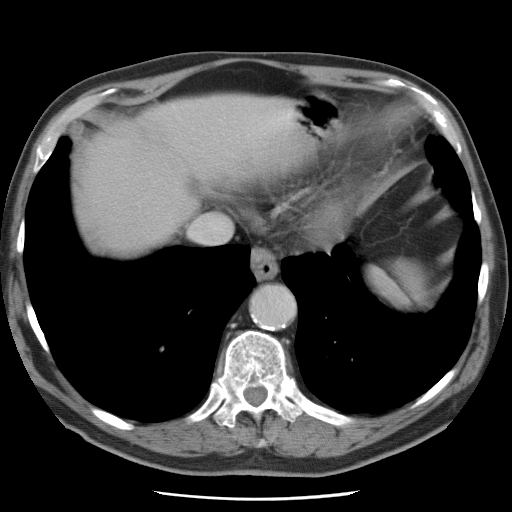
Contrast-enhanced abdominal CT, one axial slice; position 70 of 78 along the scan axis; 120 kVp; intravenous contrast given; soft-tissue window (W 400 / L 40 HU); 5 mm slice thickness; 512 × 512 image matrix, field of view 337 × 337 mm. Male patient, age 75 years. From the clinical record (not read from this slice): diagnosis: colorectal cancer liver metastases, imaged before liver resection; multiple liver metastases: yes; largest metastasis: 2.4 cm; disease in both lobes: yes.
Outlined on this slice (manually delineated by an expert):
- liver: bounding box <82,95,293,251> (left, top, right, bottom; pixels)
- planned liver remnant (the part of the liver to remain after resection): <83,154,175,254>
- liver metastasis: <185,177,204,201>